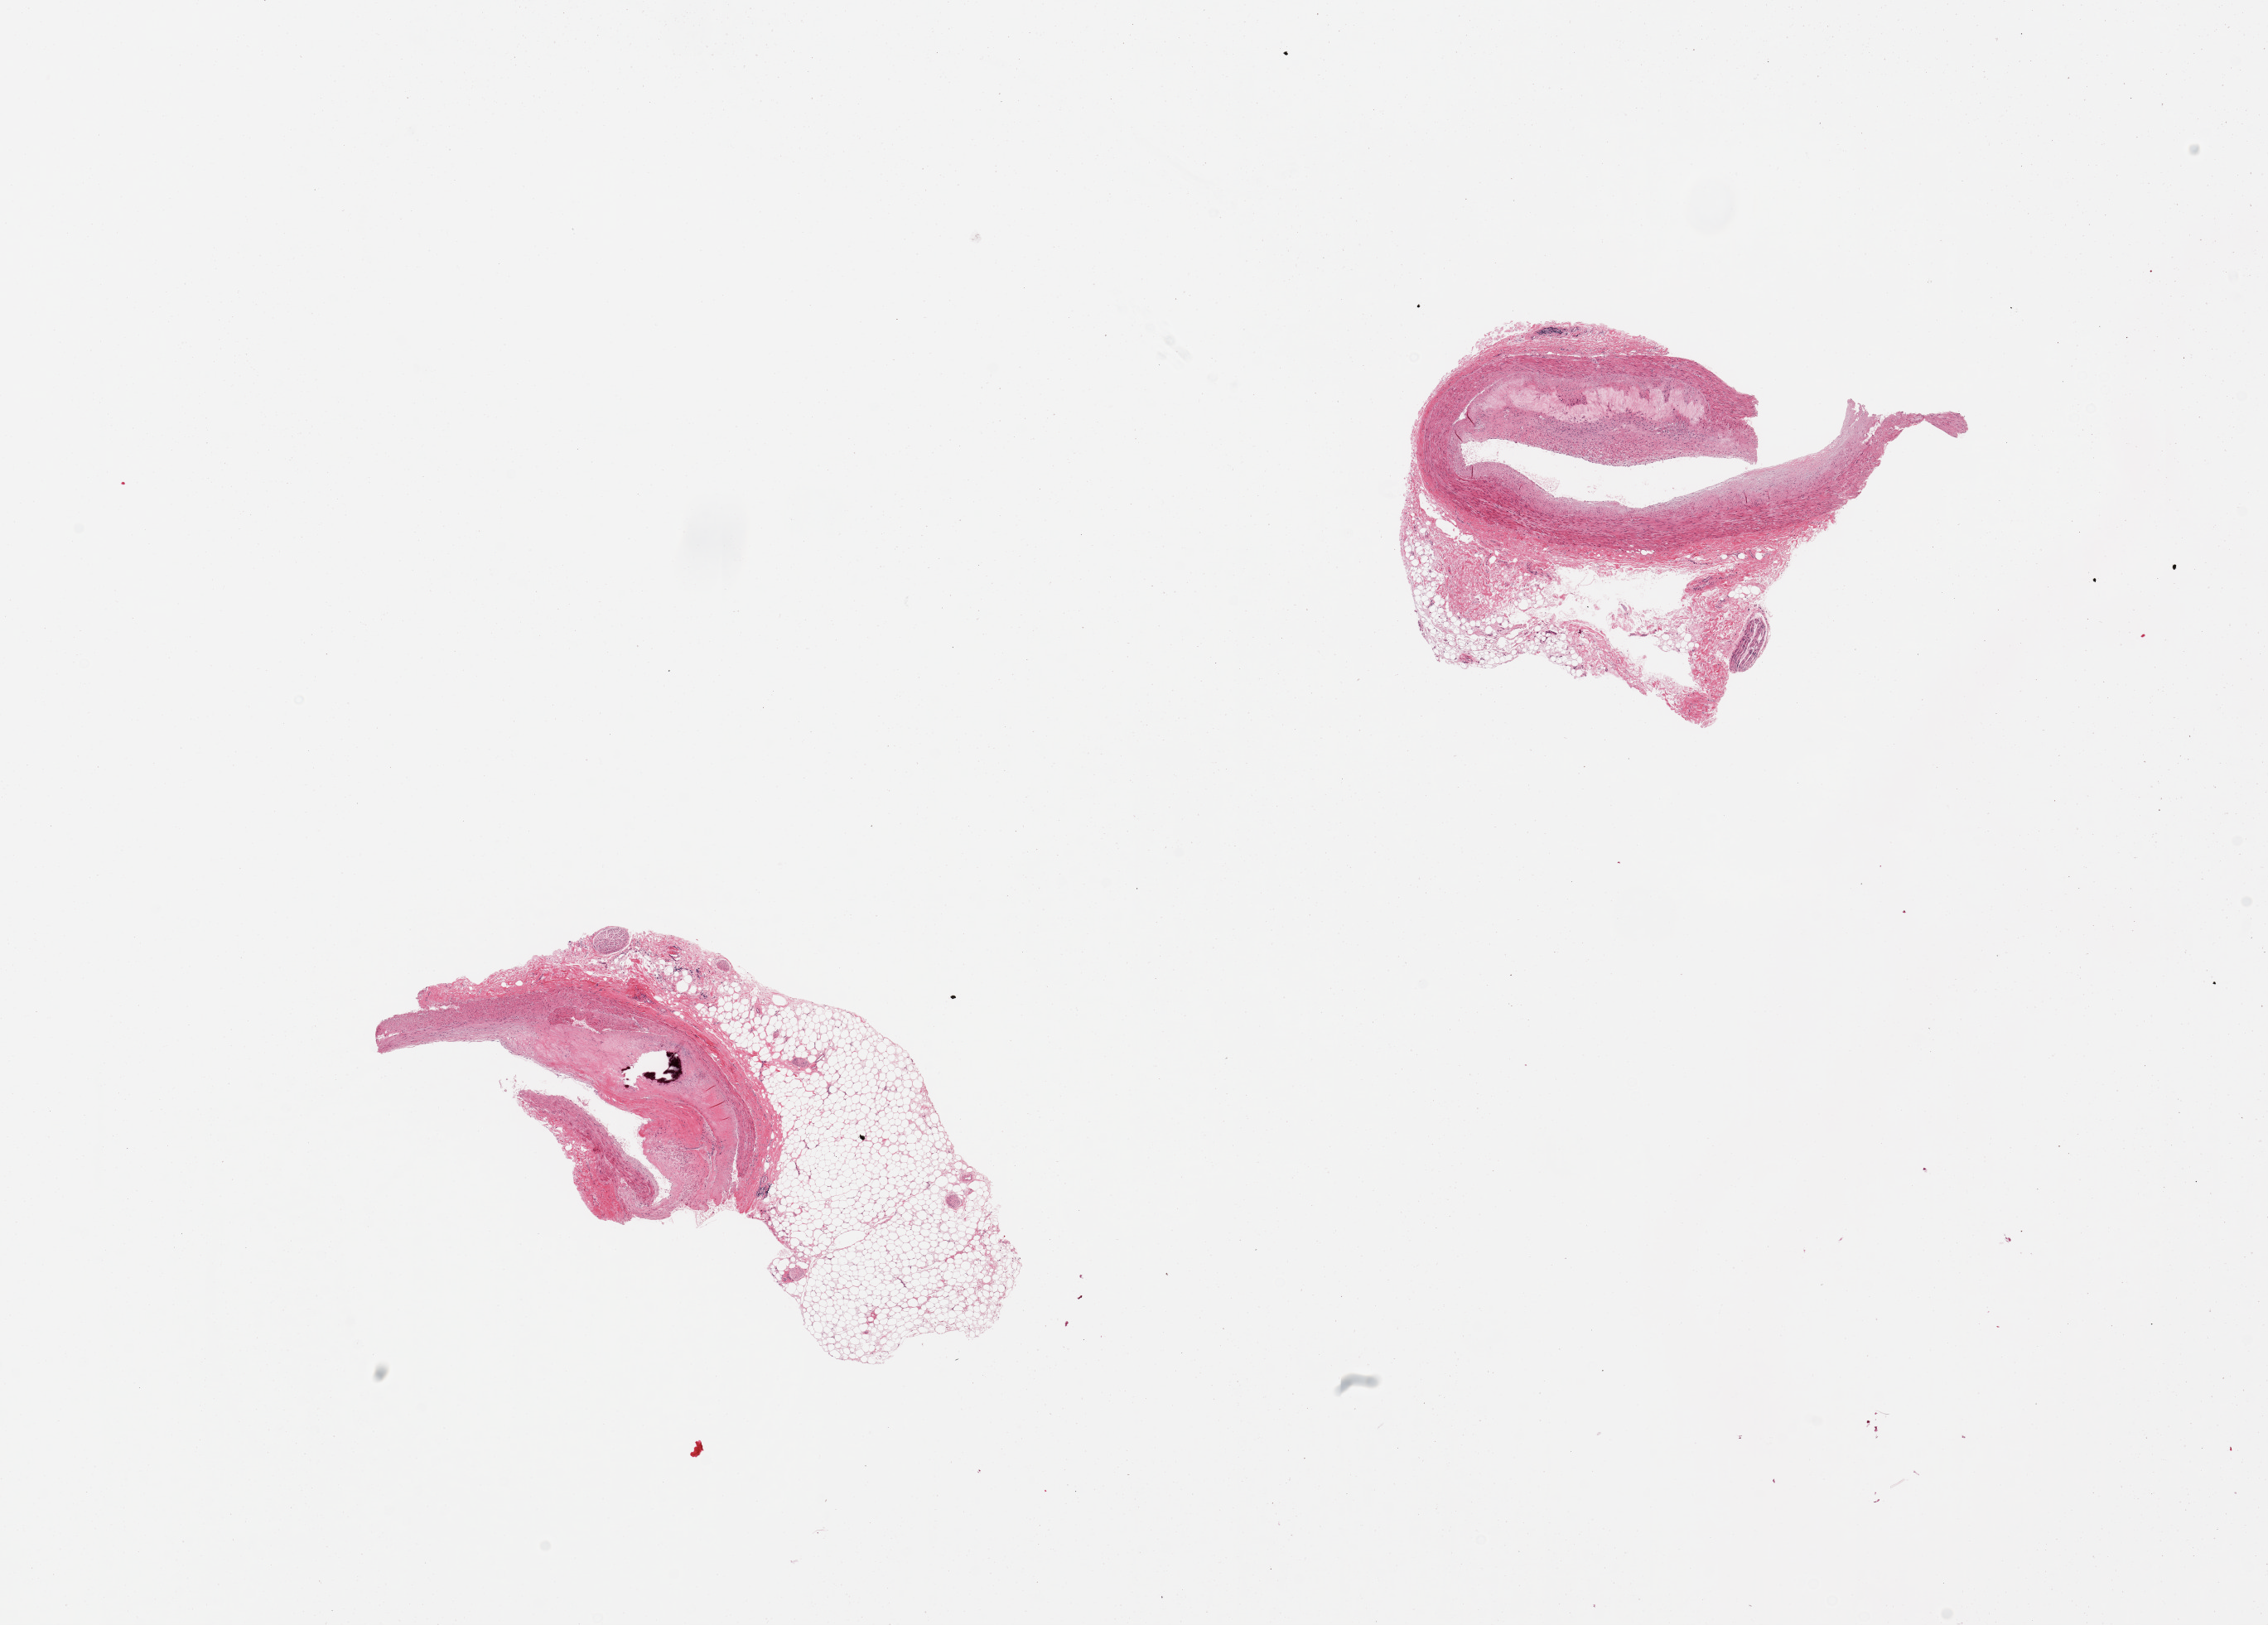
H&E whole-slide image — a low-resolution overview of the entire scanned area, about 21.7 x 15.5 mm (from a 20x scan); PAXgene-fixed paraffin-embedded (PFPE) section; section of coronary artery (target tissue); donor tissue sample.
Review note (as recorded): 2 pieces. 50% and 40% fat; moderate plaques; focal calcium.